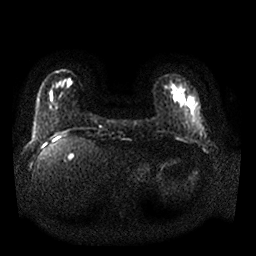
Breast MRI, one axial slice; position 4 of 25 along the scan axis; diffusion-weighted series; image 2 of 4 stored at this slice position (different b-values; order by instance number); 1.5 T; 256 × 256 image matrix, field of view 340 × 340 mm. Female patient.
Outlined on this slice (manually delineated by an expert):
- tumour on diffusion-weighted imaging: box from (x=192, y=99) to (x=198, y=109) px